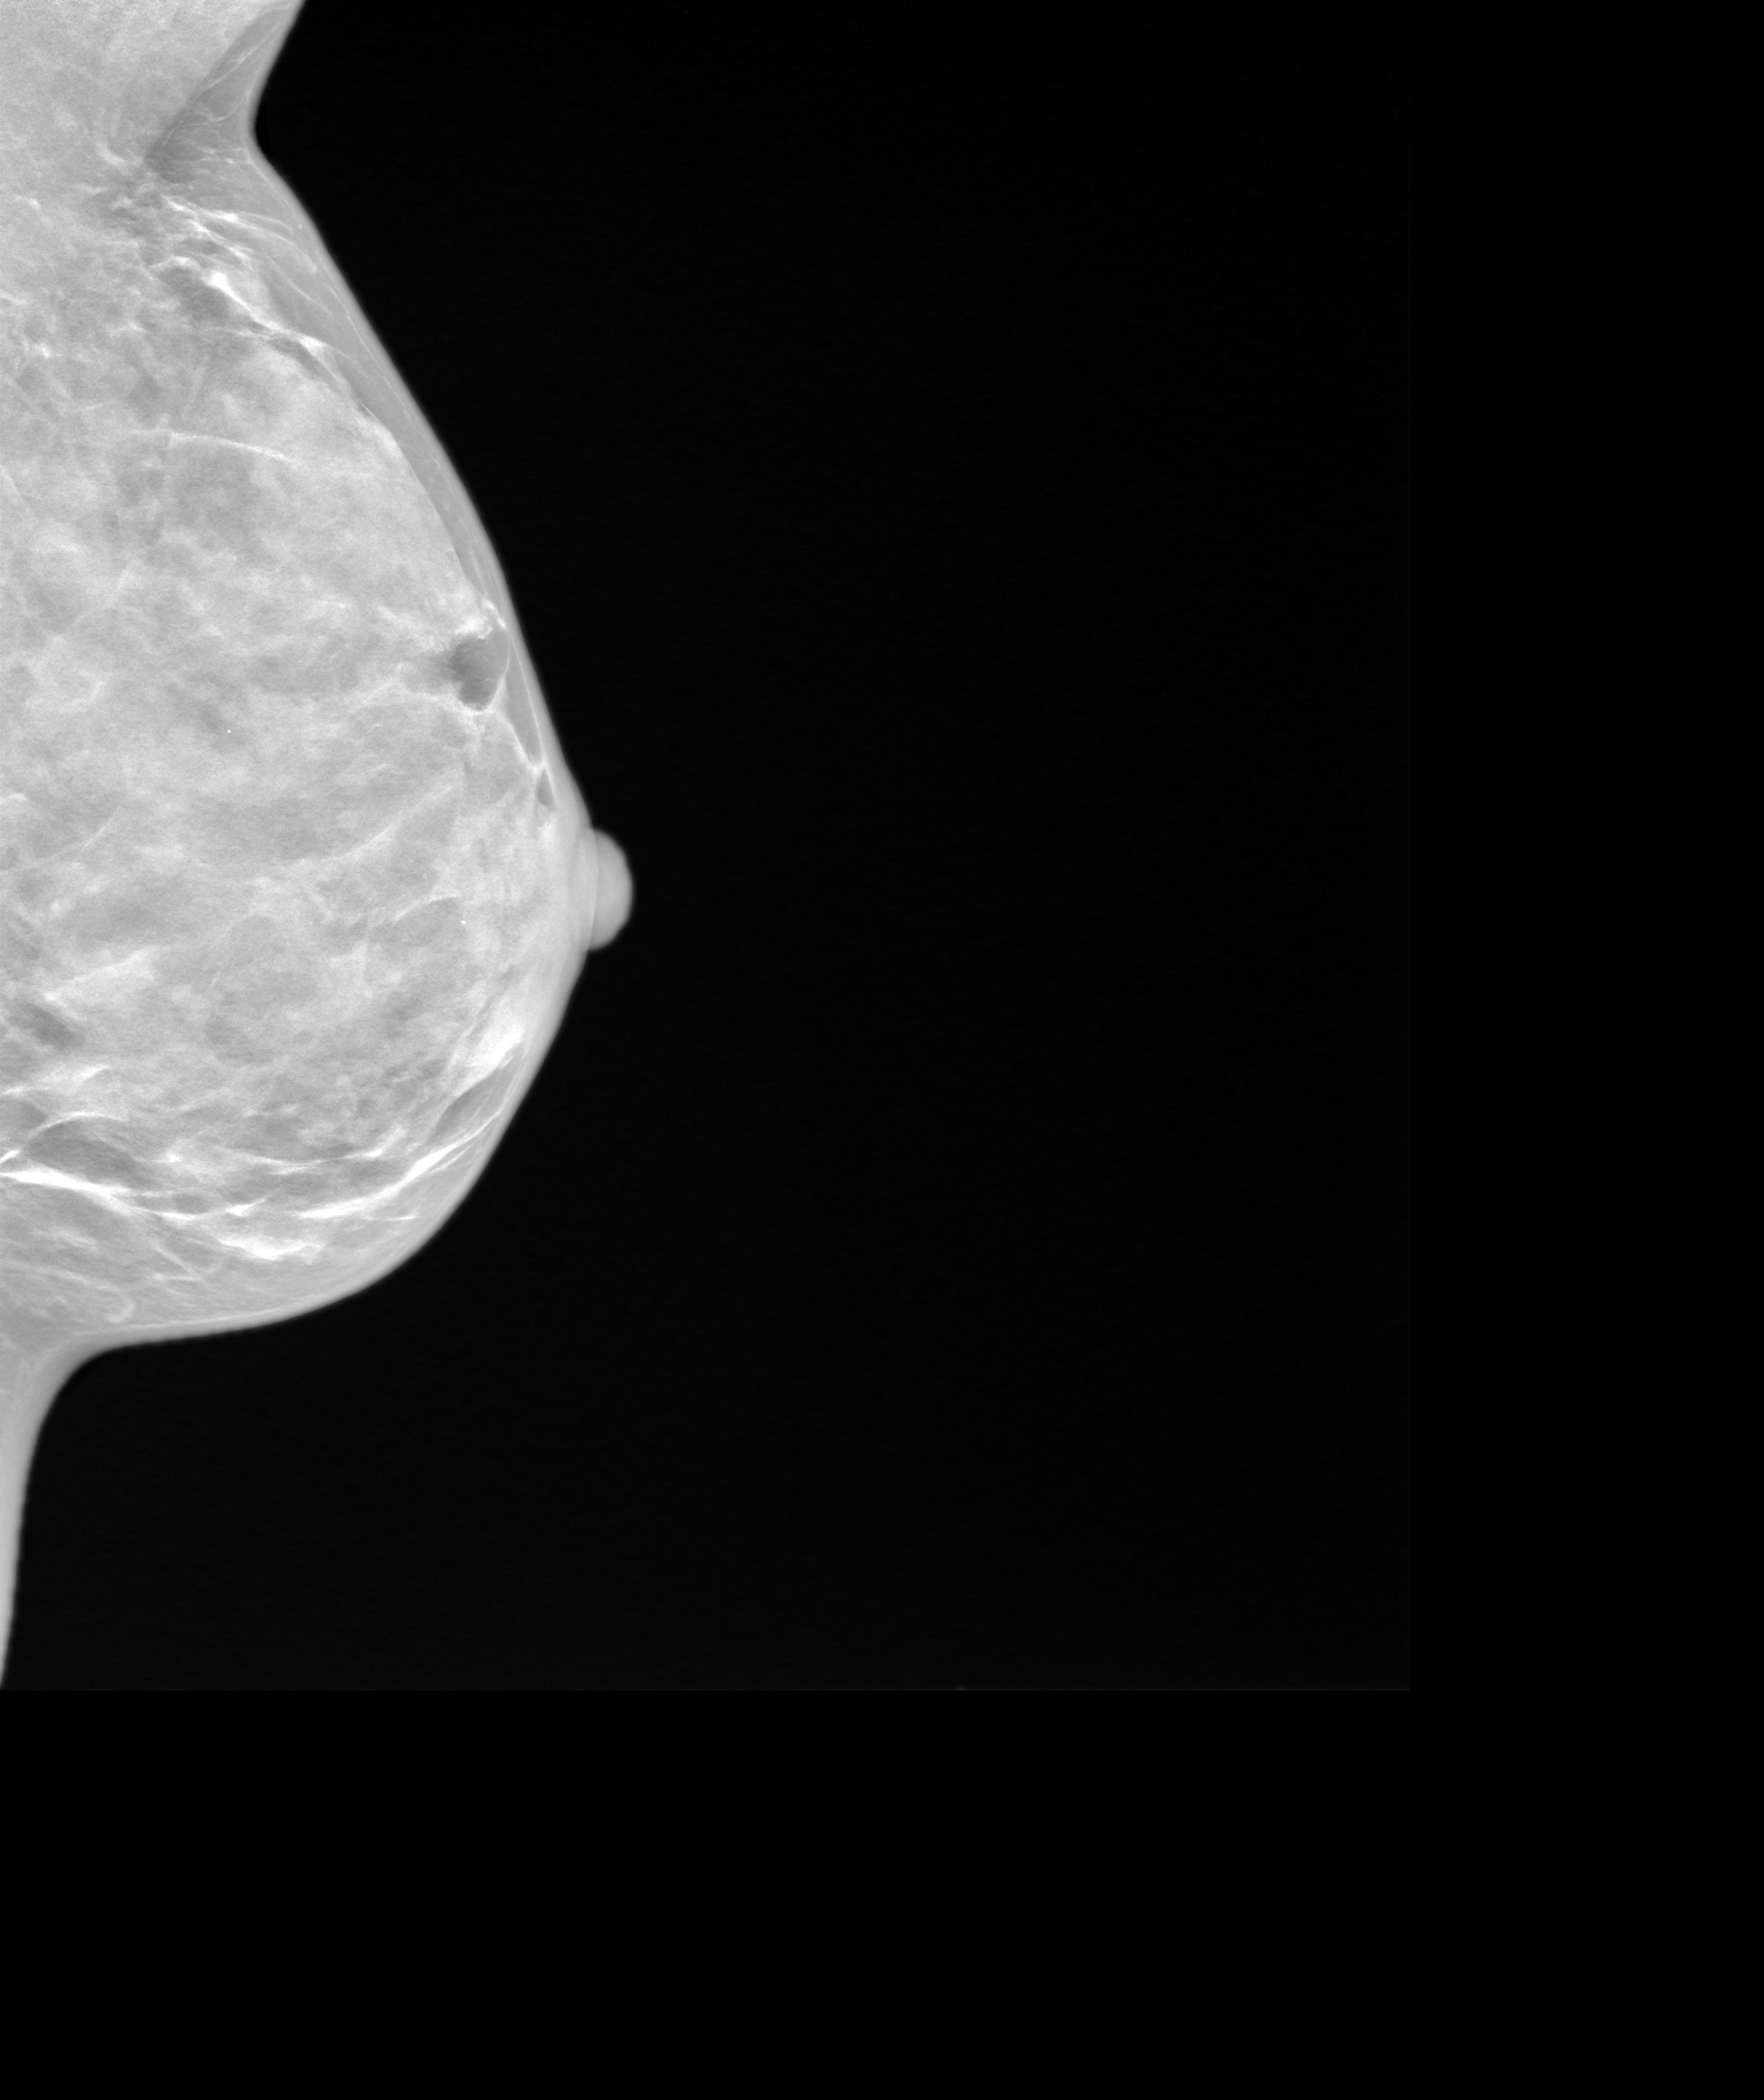
Annual screening mammography examination; system: SenoIris_1SP2(440). Patient: female, 46 years.
Image type: synthesized 2-D view from tomosynthesis. Breast: left. Projection: mediolateral oblique (MLO) view.